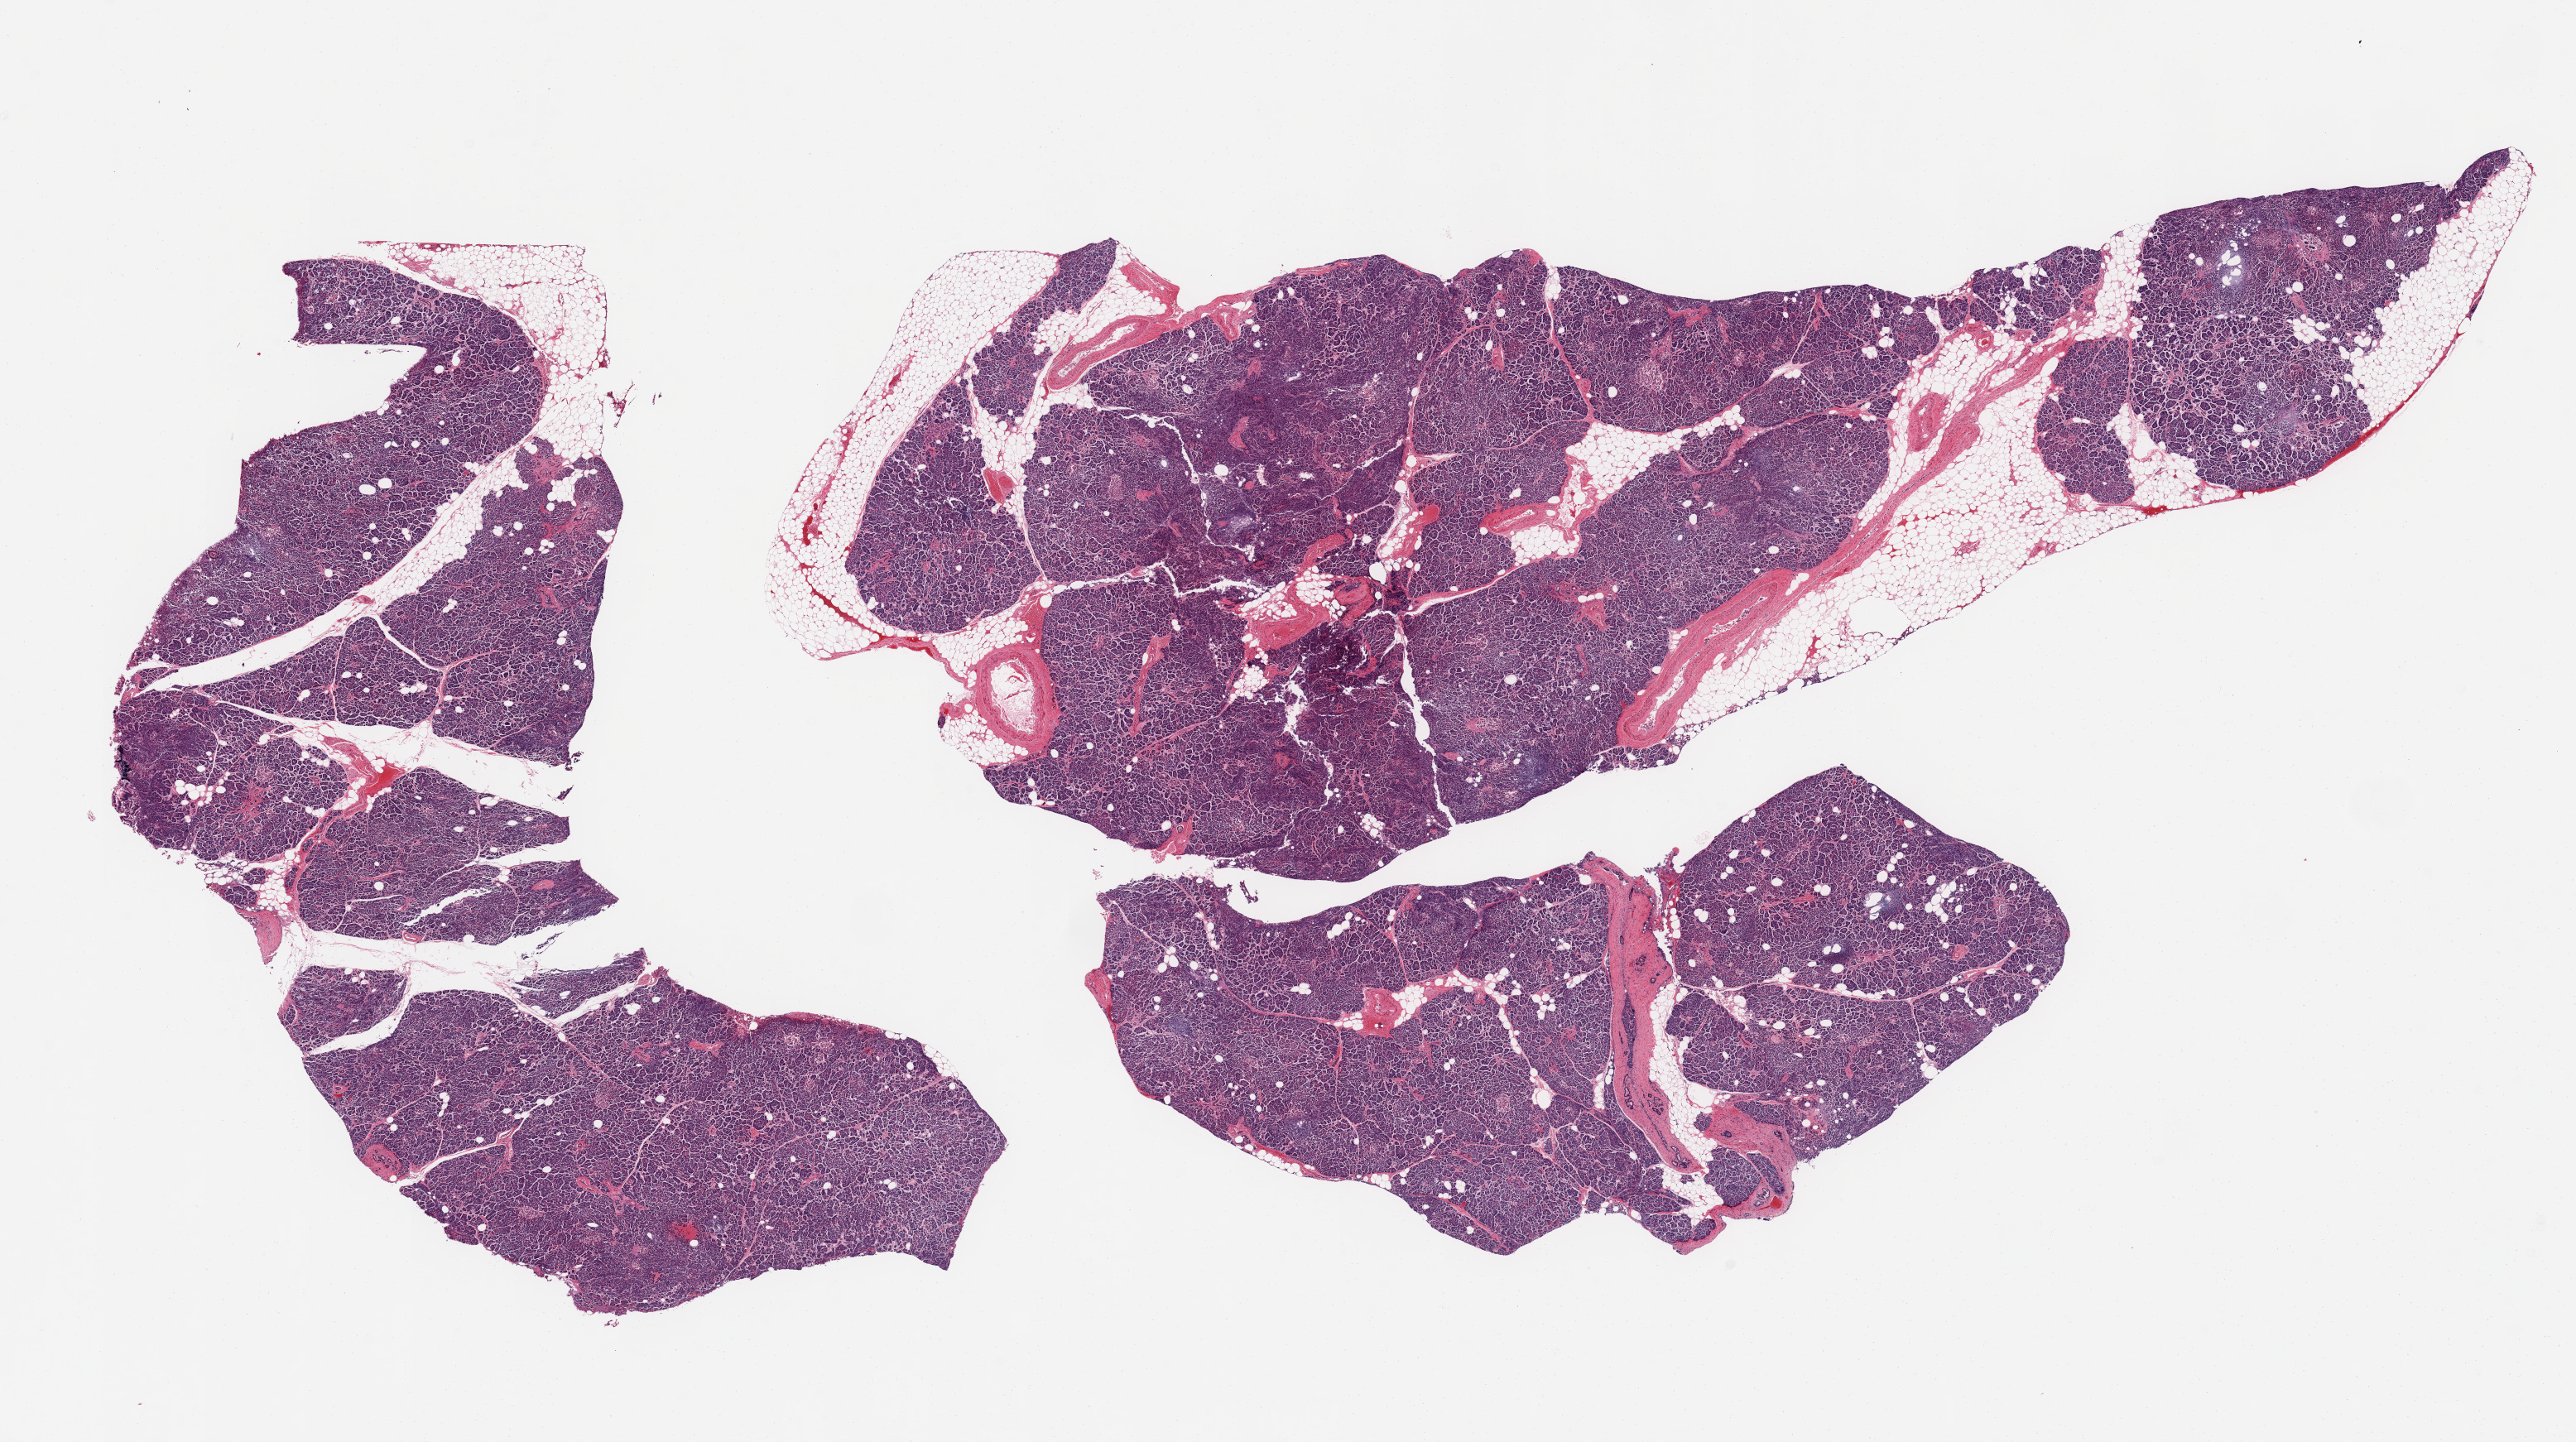
Haematoxylin and eosin whole-slide image, brightfield — whole scanned area (about 24.6 x 13.8 mm, acquisition: 20x scan) shown as a low-resolution overview, PAXgene-fixed paraffin-embedded (PFPE) section, section of pancreas (target tissue), tissue donor sample. Donor: male.
Review note (as recorded): 2 pieces, moderately advanced saponification; Islets visible but degrading.